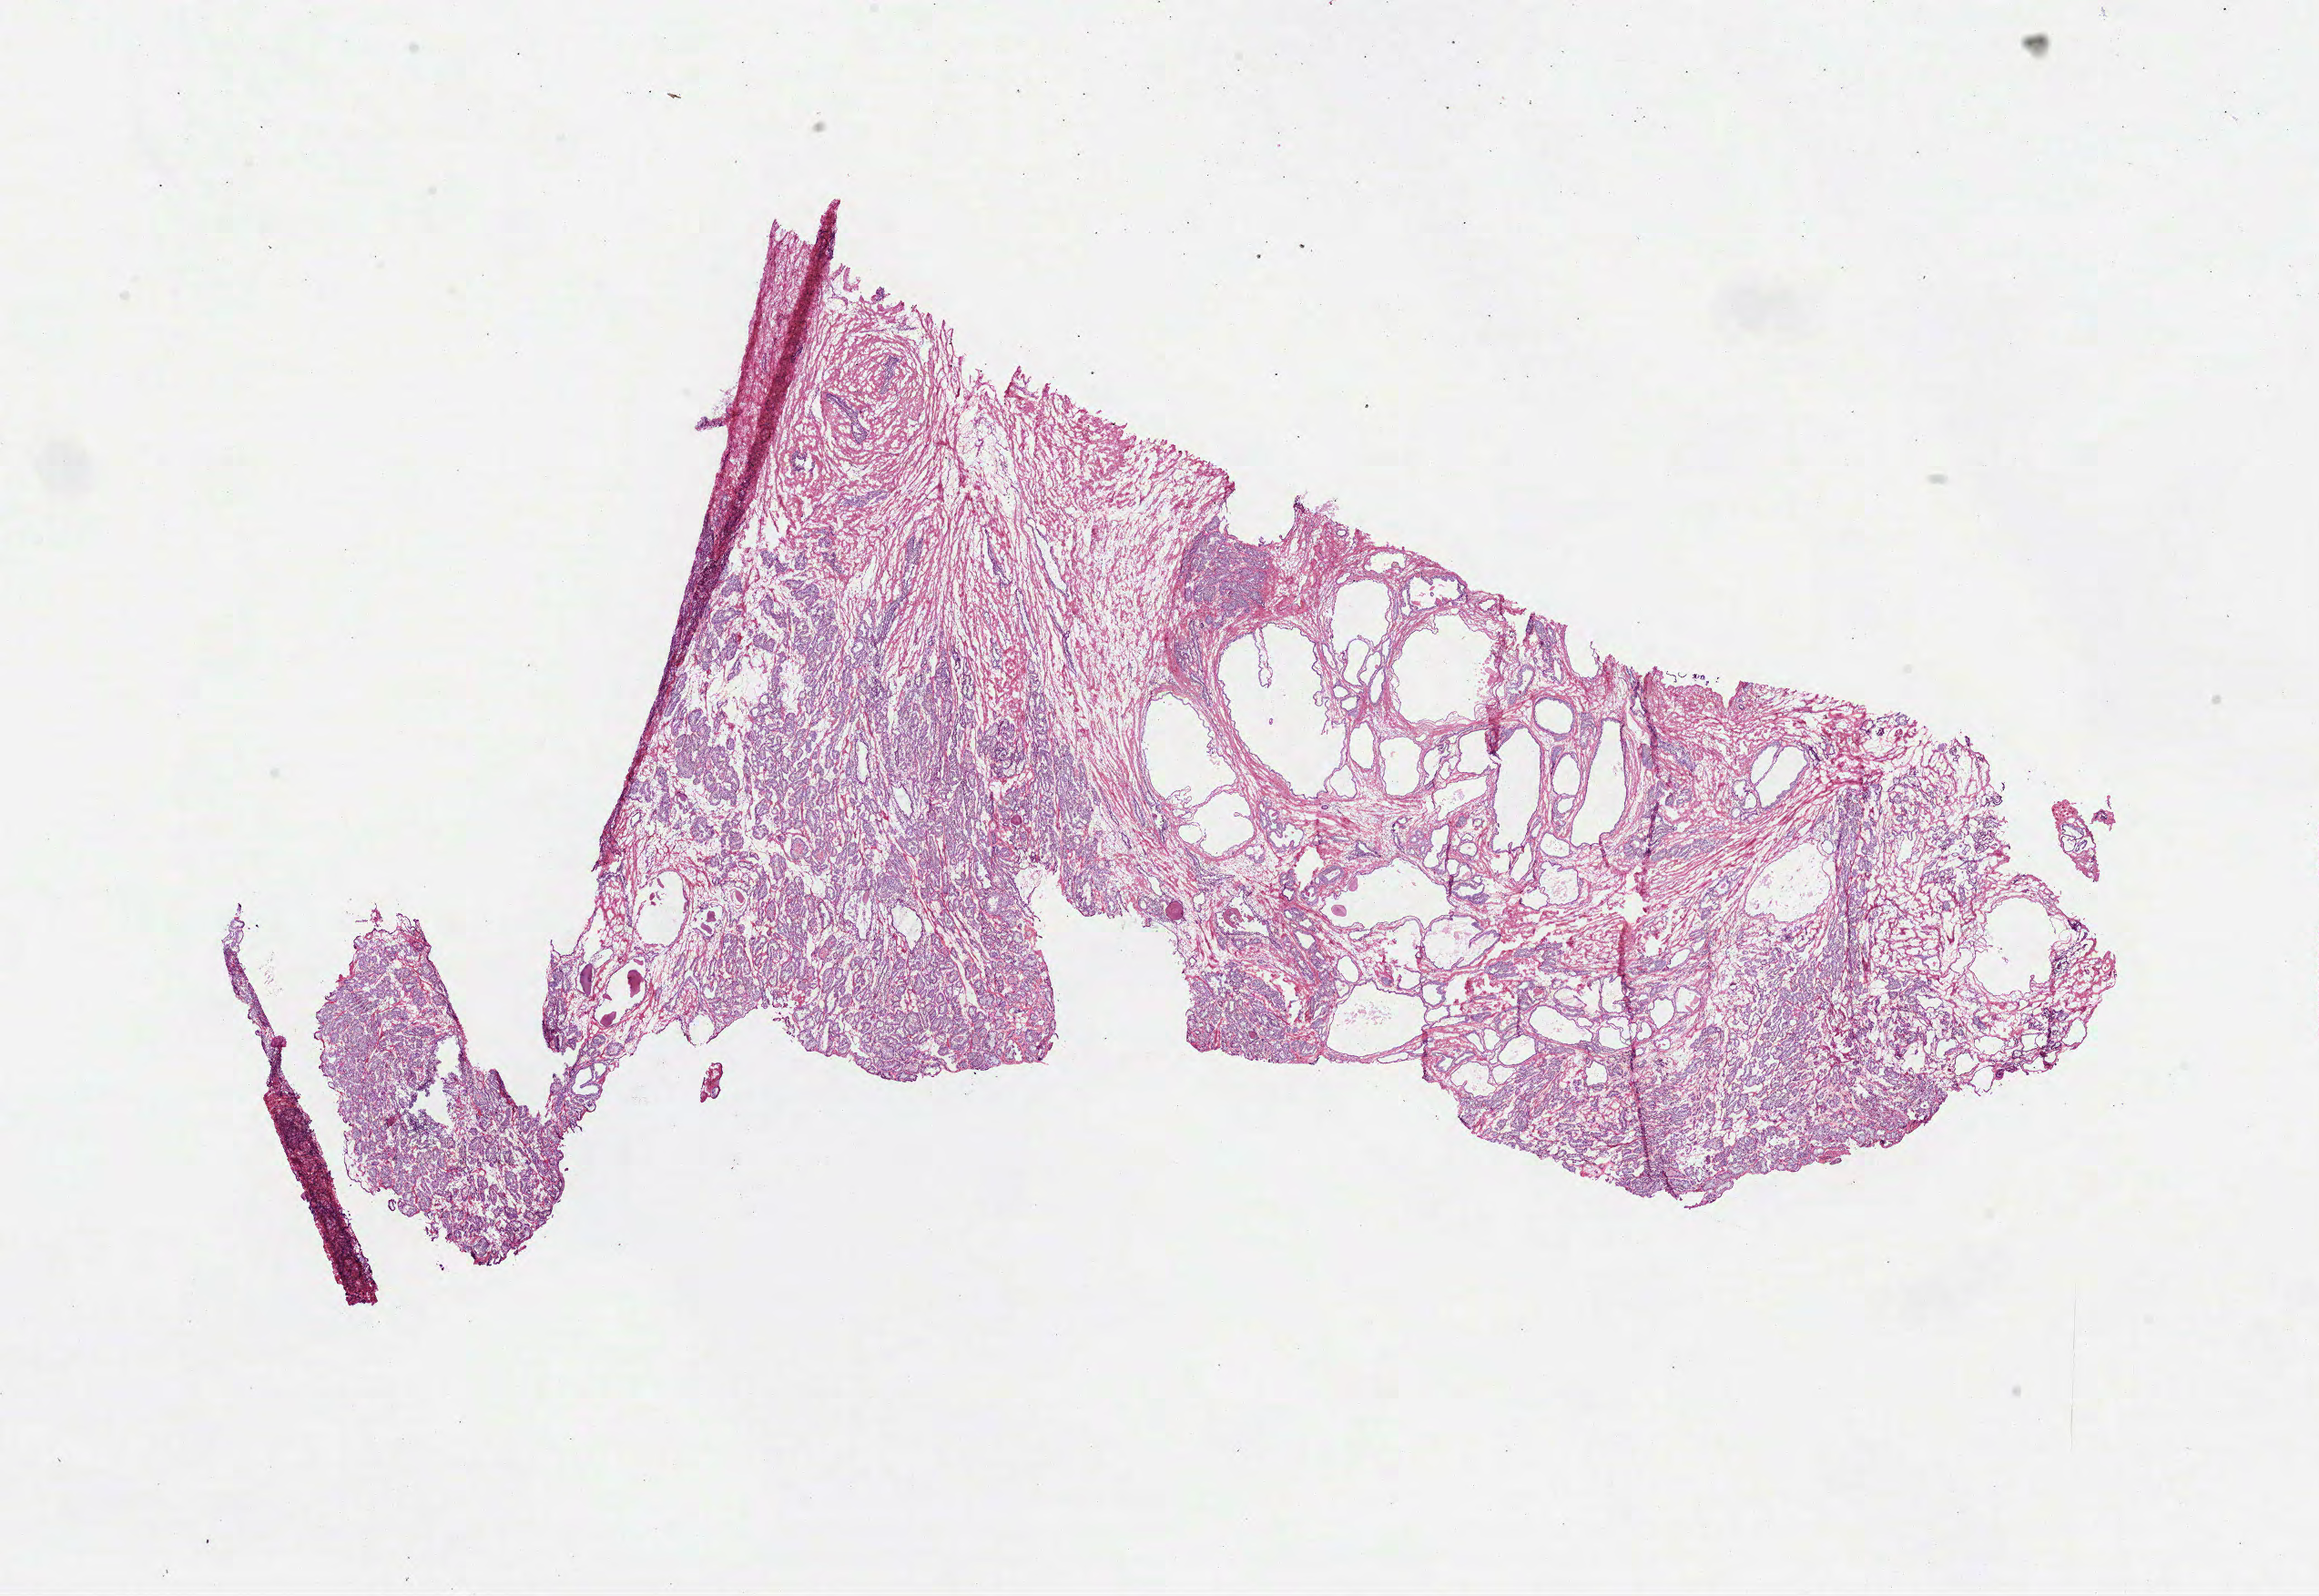
Hematoxylin and eosin (H&E) stained whole-slide image, a low-resolution overview of the entire scanned area, about 20.5 x 14.1 mm; frozen section; primary tumour sample from the prostate. Male, age 65 years at initial diagnosis. Pathologist review of this section (percent, as recorded): tumour cells 40%, tumour nuclei 60%.
Diagnosis: Acinar cell carcinoma.